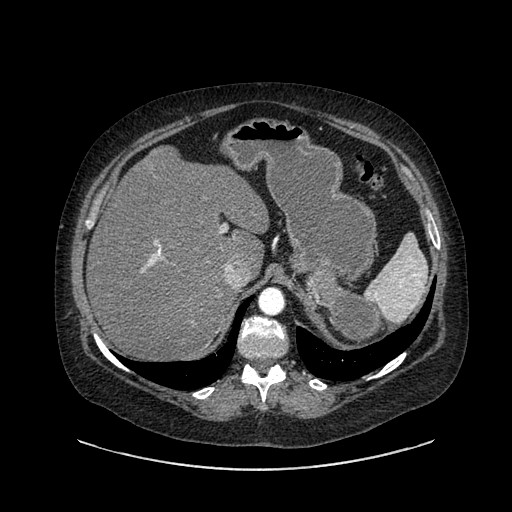
Contrast-enhanced abdominal CT, one axial slice; reconstruction kernel SOFT; intravenous contrast given; soft-tissue window (W 400 / L 40 HU); 0.62 mm slice thickness; 512 × 512 image matrix, field of view 460 × 460 mm. Female patient, age 61 years. Case-level facts recorded for this patient, not image findings: diagnosis: adrenocortical carcinoma; tumour side: left adrenal; tumour size at pathology: 13 cm; Ki-67 index: 79 %; stage (as recorded): 2.
Outlined on this slice (semi-automatic segmentation, software-assisted and operator-edited):
- mass: bounding box (x1, y1, x2, y2) in pixels: (304, 268, 380, 344)